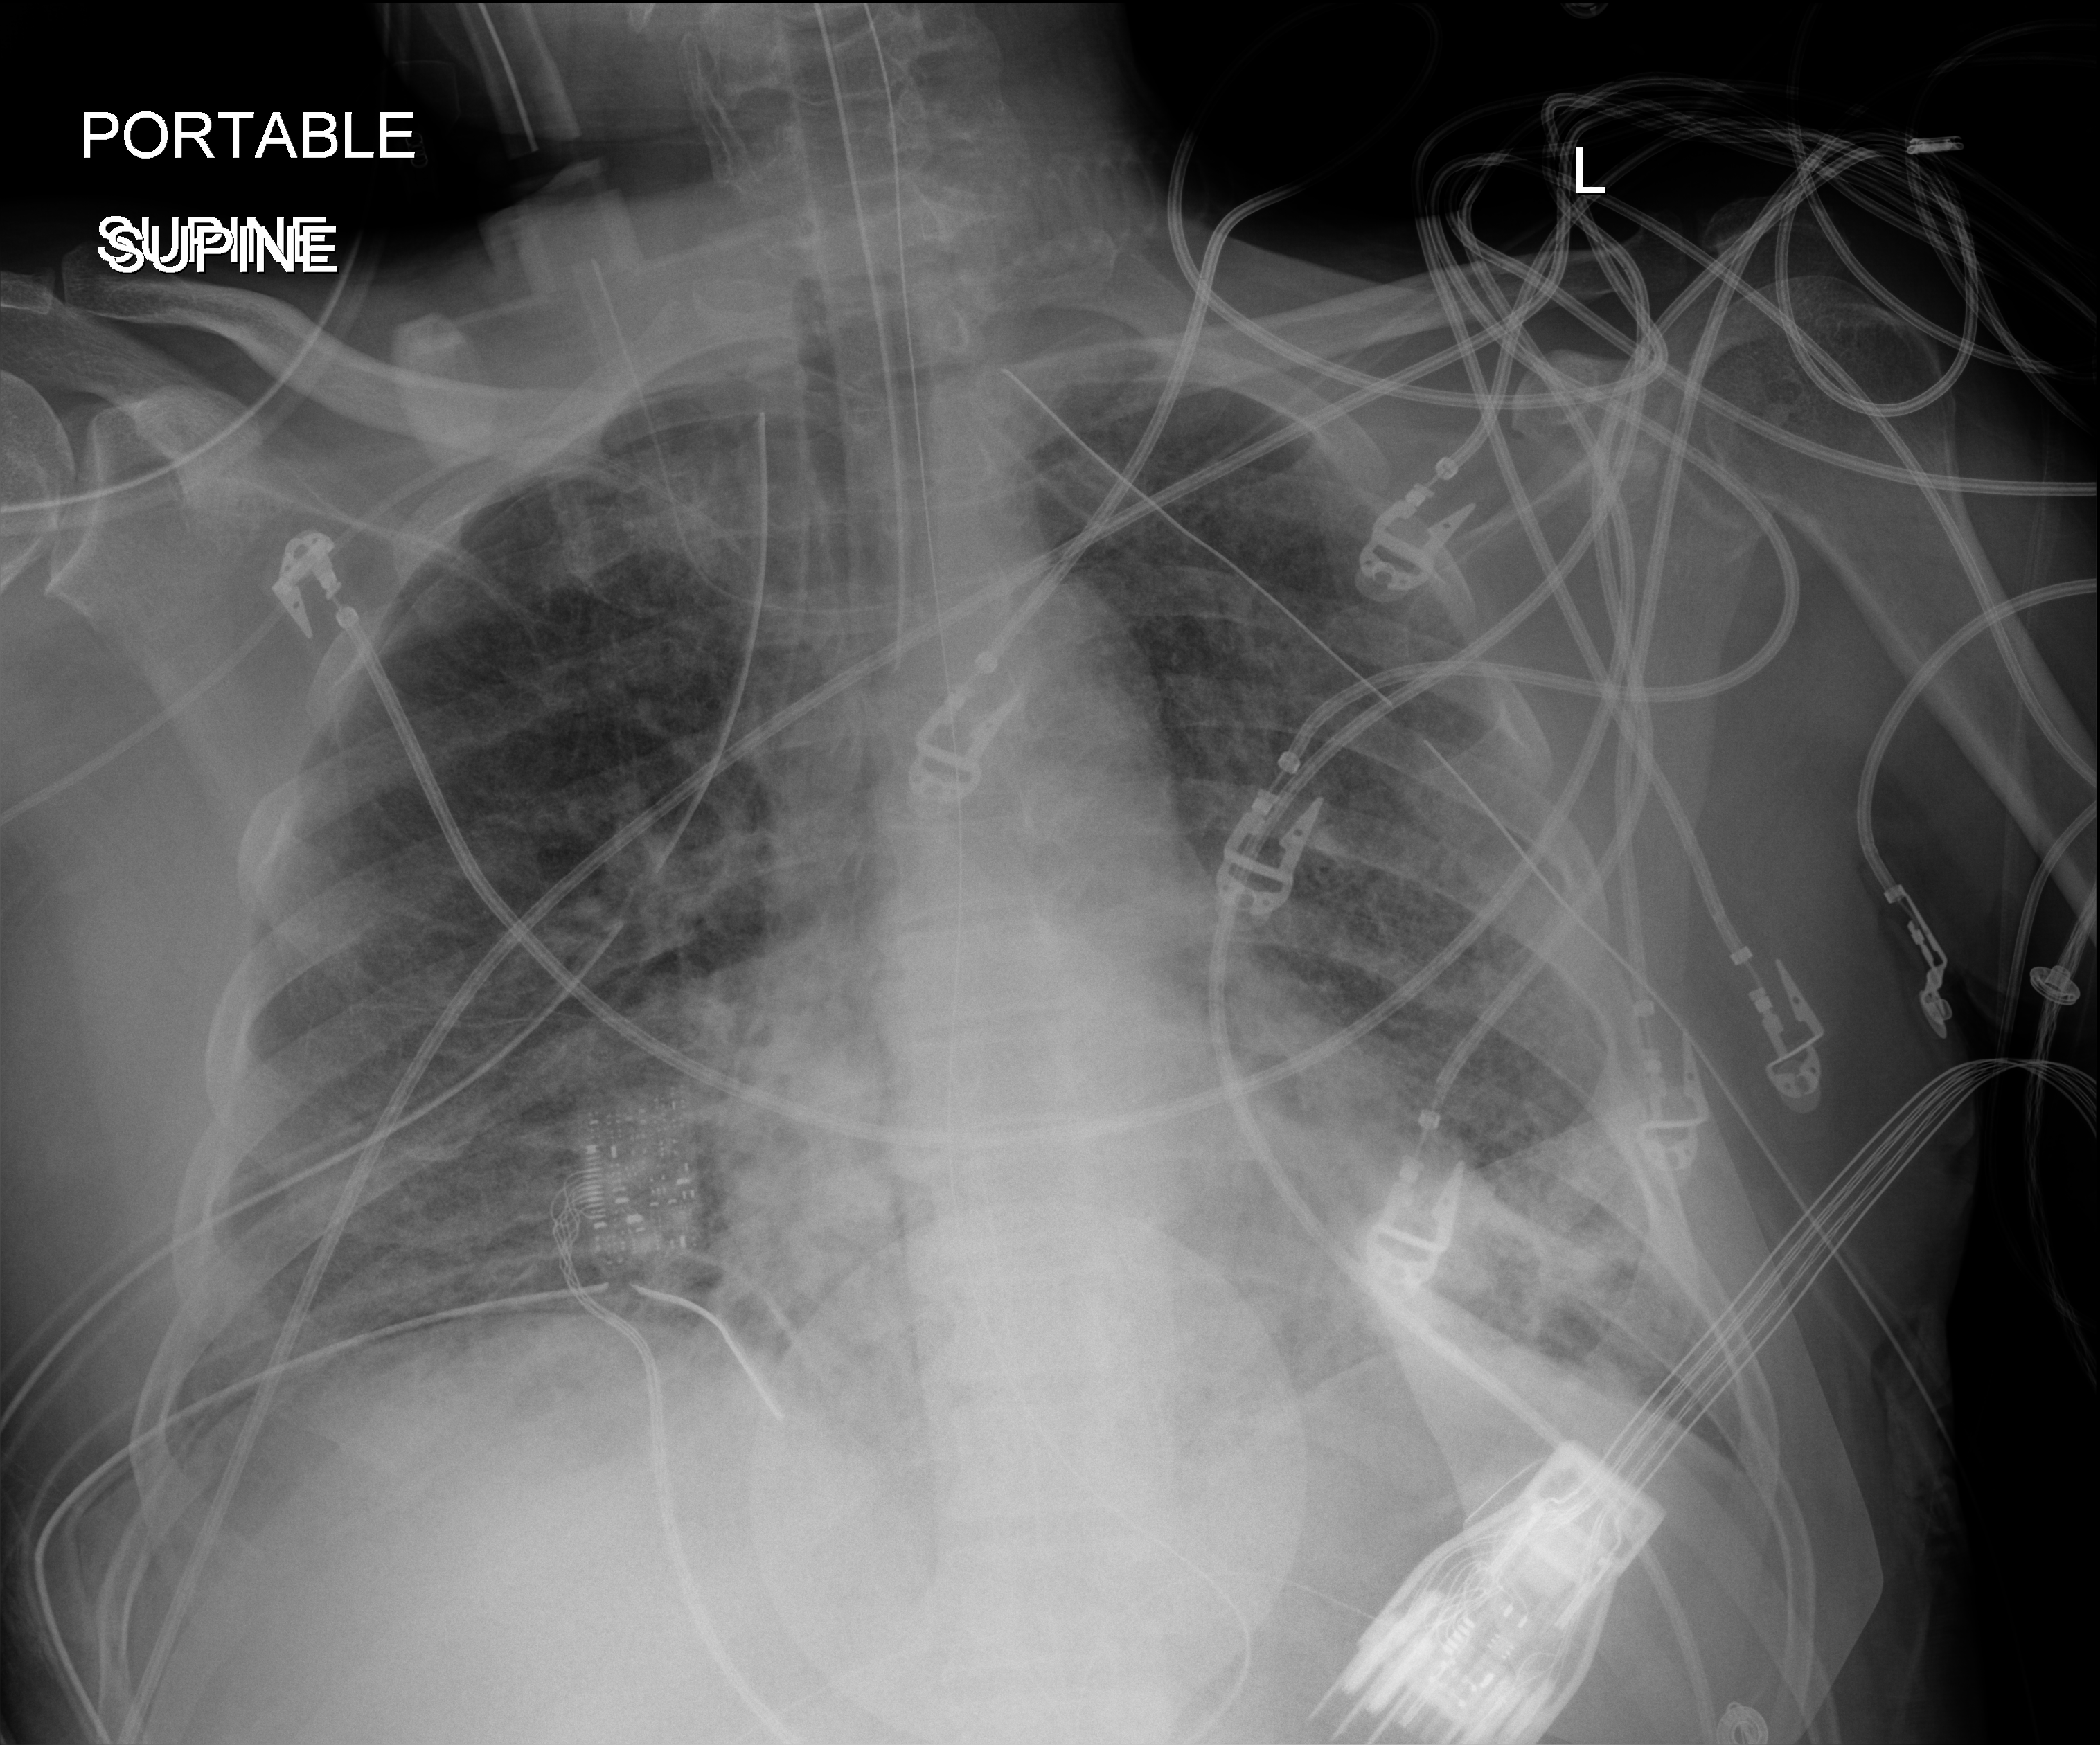
Bedside chest radiograph (digital radiography), anteroposterior (AP) projection. Patient hospitalised with COVID-19; male, aged 18–59 years.
From the hospital-stay record, not from the radiograph (when in the stay this image was taken is not recorded):
- admitted to intensive care during this hospital stay: yes
- mechanically ventilated during this hospital stay: yes